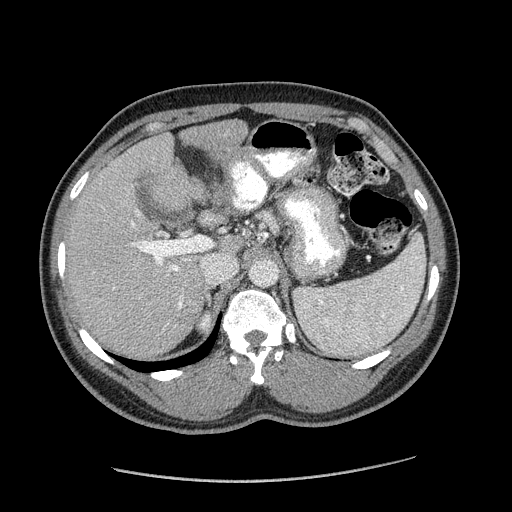
Contrast-enhanced abdominal CT (liver protocol), one axial slice. Reconstruction kernel STANDARD. Soft-tissue window (W 400 / L 40 HU). 2.5 mm slice thickness. 512 × 512 image matrix. Case-level facts recorded for this patient, not image findings: diagnosis: hepatocellular carcinoma (patient treated with transarterial chemoembolisation; whether this scan precedes or follows treatment is not stated here); TNM stage (as recorded): Stage-I; Child-Pugh class: A; tumour differentiation: well differentiated; tumour size: 3.1 cm.
Annotated regions visible in this slice (semi-automatically segmented with operator editing):
- liver parenchyma outside the tumour (the mass and vessels are separate outlines, so this box may not span the whole liver): box from (x=66, y=120) to (x=248, y=358) px
- liver vessels: (x=131, y=210)–(x=183, y=309)